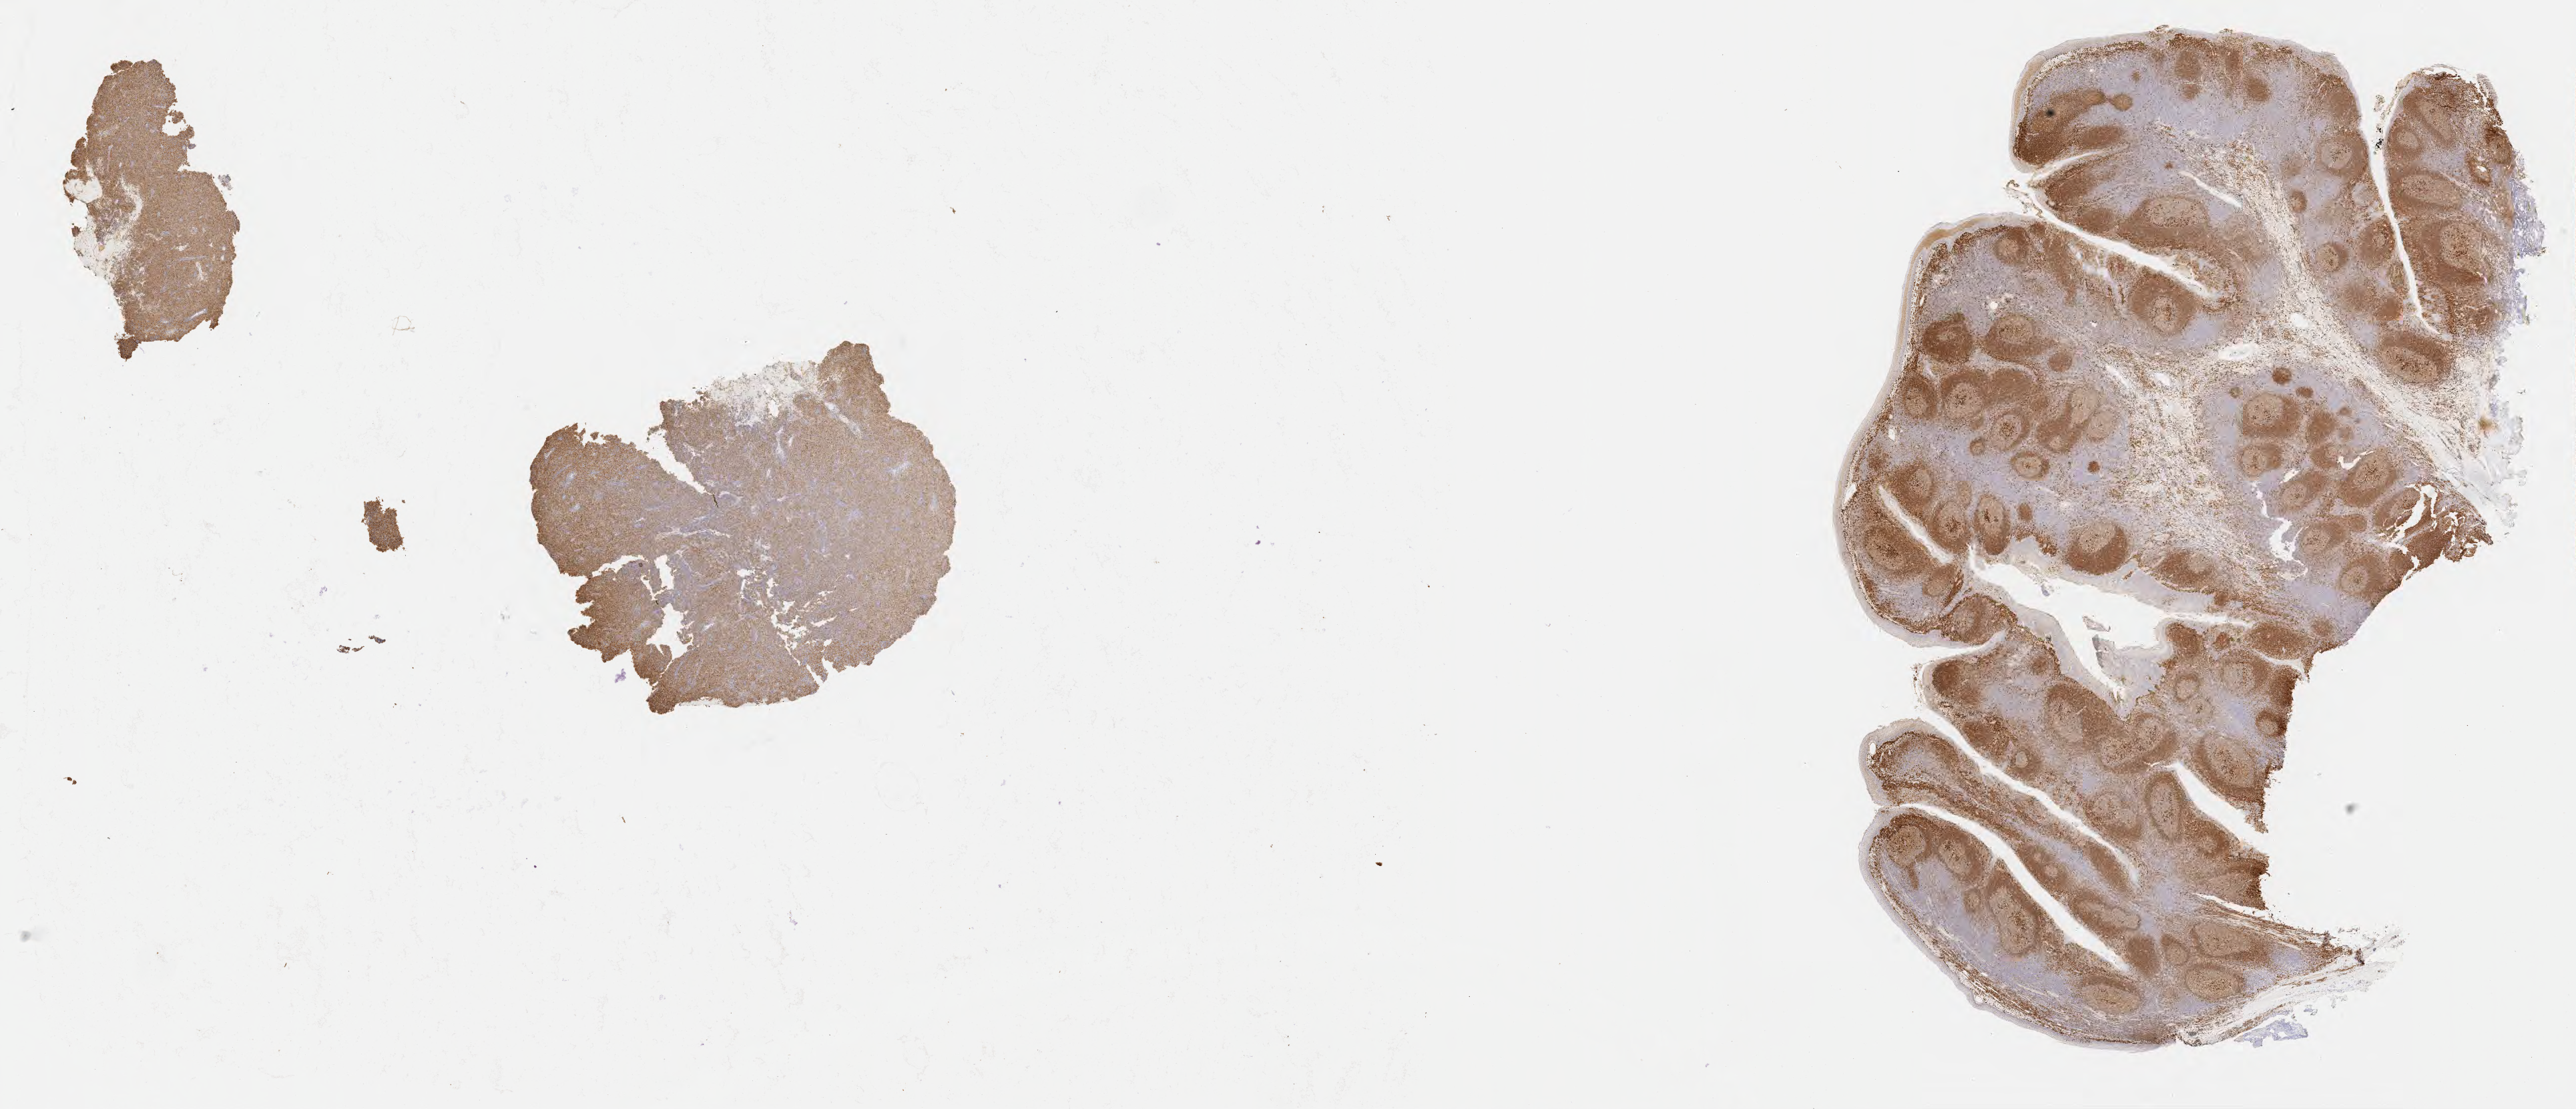
Immunohistochemistry (IHC) whole-slide image stained for CD79a, shown as a low-resolution overview of the whole scanned area (about 31.2 x 13.4 mm); specimen: tumor tissue; site: lymph node. Female patient, aged 51.
- histologic diagnosis: Diffuse large B-cell lymphoma, NOS